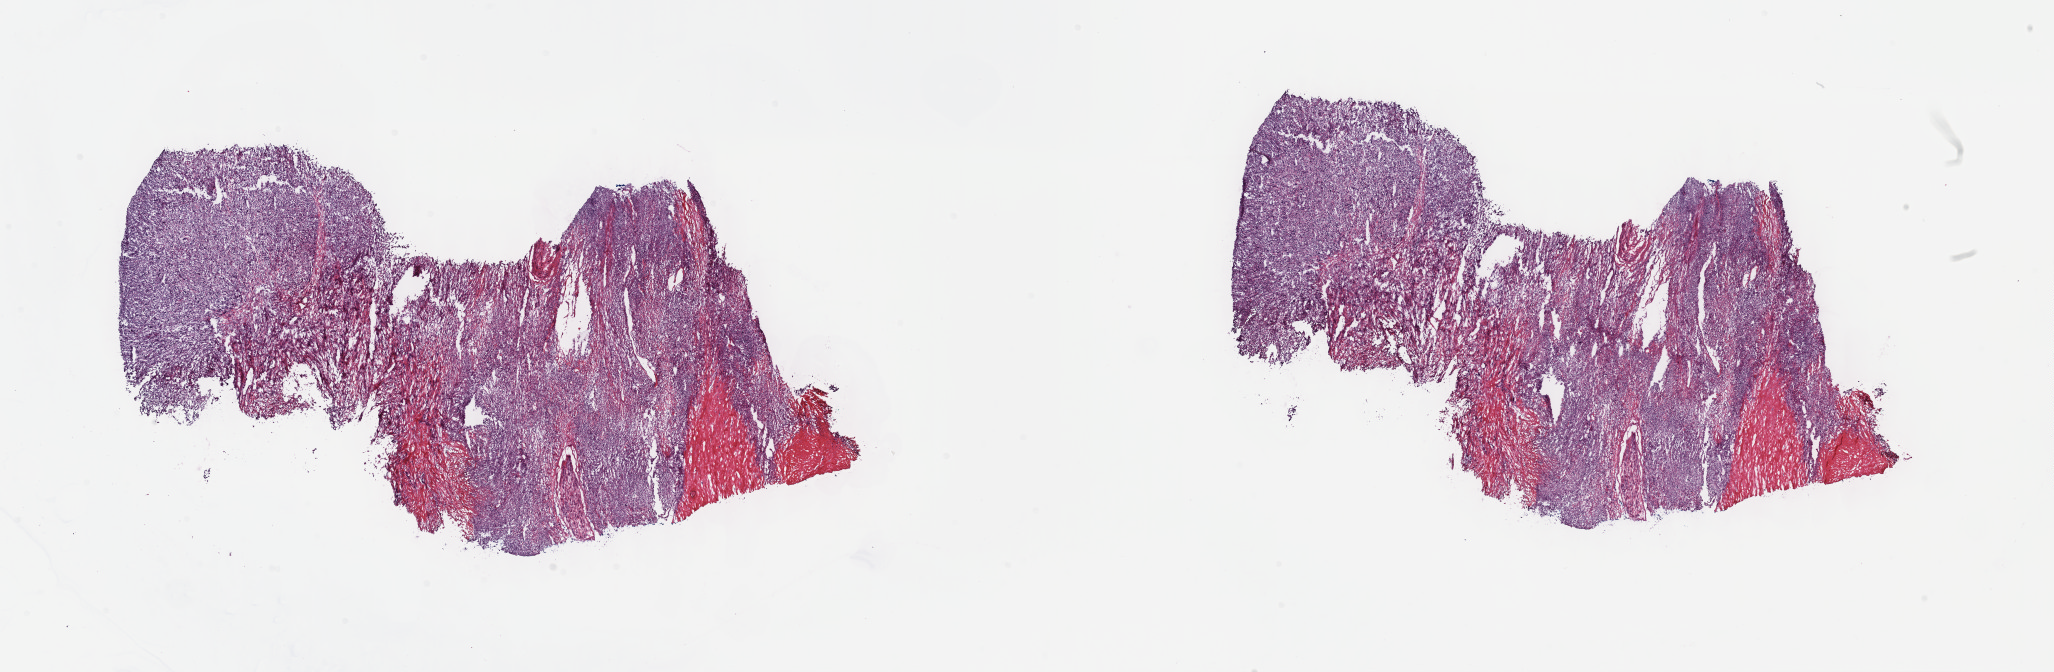
Digitized H&E-stained tissue section (whole slide) — low-resolution overview of the scanned area, about 33.2 x 10.9 mm. Frozen section. Primary tumour sample from the connective, subcutaneous and other soft tissues. Patient: male, age at initial diagnosis 76 years. Slide review estimates, as recorded: tumour cells 75%, tumour nuclei 95%, normal cells 15%, stromal cells 10%, necrosis 0%. Inflammatory infiltration, as recorded: lymphocyte infiltration 0%, monocyte infiltration 0%, neutrophil infiltration 0%.
Diagnosis: Malignant fibrous histiocytoma (connective, subcutaneous and other soft tissues of thorax).